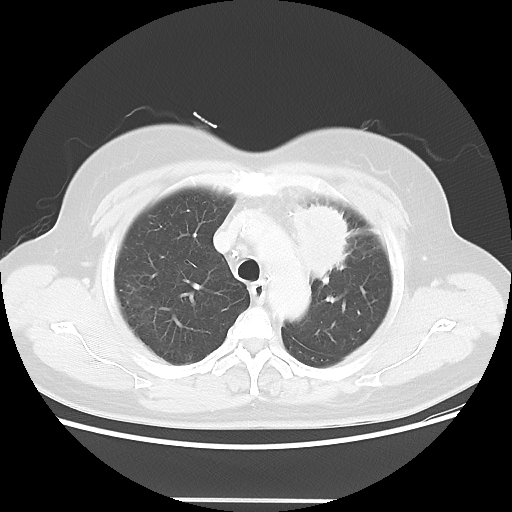
Chest CT, one axial slice; slice 42 of 52 in the series (ordered by position); reconstruction kernel LUNG; 120 kVp; lung window (W 1500 / L -600 HU); 512 × 512 image matrix, field of view 382 × 382 mm. Patient: female, 52 years. Case-level facts recorded for this patient, not image findings: clinical TNM (as recorded): T2 N3 M0.
Annotated regions visible in this slice (rectangle marked by the reading radiologist):
- lung tumour (recorded histology: adenocarcinoma): bounding box [x1, y1, x2, y2] px = [289, 198, 354, 278]